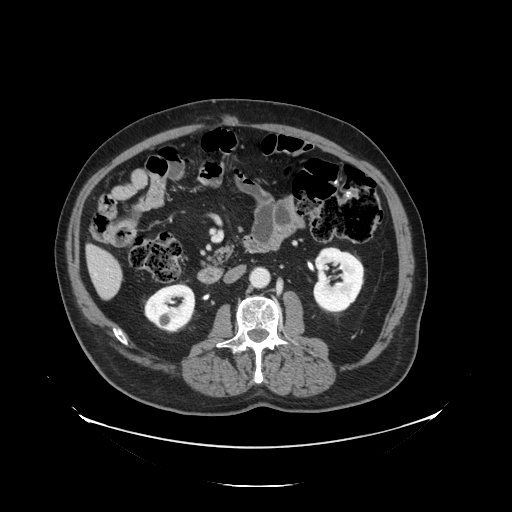
Contrast-enhanced abdominal CT, one axial slice. Slice 40 of 138 in the series (ordered by position). Reconstruction kernel STANDARD. Intravenous contrast given. Soft-tissue window (W 400 / L 40 HU). 512 × 512 image matrix, field of view 497 × 497 mm. Male patient, age 77 years. From the clinical record (not read from this slice): diagnosis: colorectal cancer liver metastases, imaged before liver resection; multiple liver metastases: no; largest metastasis: 1.5 cm.
Structures marked on this image (manually delineated by an expert):
- liver: bounding box (x1, y1, x2, y2) in pixels: (89, 247, 123, 299)
- planned liver remnant (the part of the liver to remain after resection): (89, 247, 119, 276)